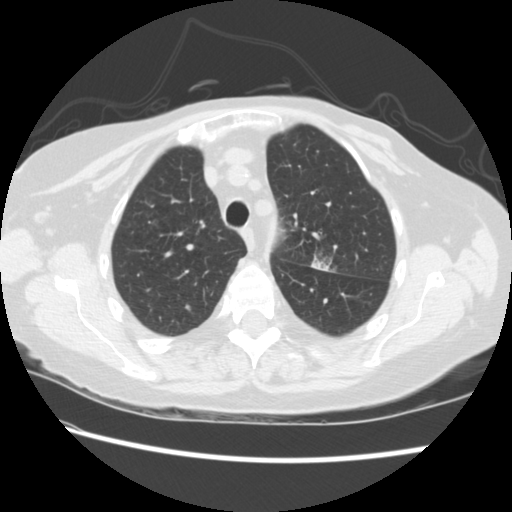
Low-dose screening chest CT, axial slice, baseline screening round, lung window (W 1500 / L -600 HU), standard (soft-tissue) reconstruction kernel (STANDARD), 120 kVp, slice 59 of 224 in the series, 512 × 512 image matrix. Female, age 74 years at enrolment. Former smoker at enrolment.
Lesion marked by an expert reader, bounding box <296,235,346,279> (left, top, right, bottom; pixels). The screening reader recorded 2 non-calcified nodules or masses ≥4 mm on this exam (left upper lobe, right lower lobe); which of them this box marks is not recorded. Later outcome: lung cancer diagnosed 309 days after this screen — non-small cell carcinoma, left upper lobe, stage IV (AJCC 6th edition).